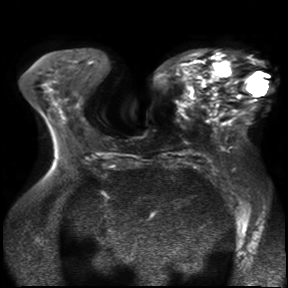
Breast MRI, one axial slice. Slice 14 of 30 in the series (ordered by position). Diffusion-weighted series; image 2 of 4 stored at this slice position (different b-values; order by instance number). 3 T. 4 mm slice thickness. 288 × 288 image matrix, field of view 360 × 360 mm. Female patient.
Outlined on this slice (outlined manually by an expert reader):
- tumour on diffusion-weighted imaging: bounding box [x1, y1, x2, y2] px = [209, 60, 232, 78]